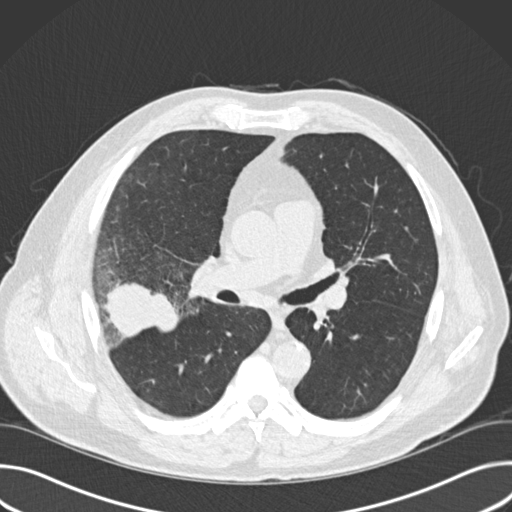
Low-dose screening chest CT, one axial slice. Slice 95 of 157 in the series (ordered by position). 120 kVp. Lung window (W 1500 / L -600 HU). 2 mm slice thickness. 512 × 512 image matrix, field of view 380 × 380 mm.
Outlined on this slice (manually delineated by an expert):
- lesion 1 (tumor, upper lobe of right lung): bounding box [x1, y1, x2, y2] px = [105, 283, 180, 338]